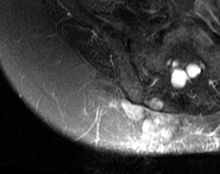
MRI of an extremity soft-tissue mass, one axial slice; slice 46 of 63 in the series (ordered by position); T2-weighted fat-saturated; MR volume resampled by the dataset authors to the PET/CT grid (not the native acquisition matrix); 3.27 mm slice thickness; 220 × 174 image matrix, field of view 215 × 170 mm. Female patient. Case-level facts recorded for this patient, not image findings: histological type: spindle cell suggestive of myxofibrosarcoma; grade: intermediate; site of the primary tumour: right buttock.
Outlined on this slice (expert contour drawn on MRI and transferred to this co-registered scan by the dataset authors):
- gross tumour volume (mass): bounding box (x1, y1, x2, y2) in pixels: (111, 98, 178, 138)